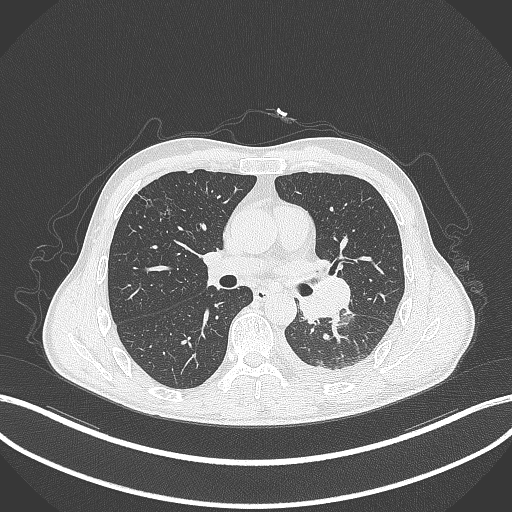
Chest CT, one axial slice. Position 178 of 295 along the scan axis. Reconstruction kernel B70f. Lung window (W 1500 / L -600 HU). 1 mm slice thickness. 512 × 512 image matrix, field of view 400 × 400 mm. Patient: male, 47 years. Case-level facts recorded for this patient, not image findings: clinical TNM (as recorded): T3 N1 M1c; histopathological grade: G3.
Outlined on this slice (bounding box drawn by a radiologist):
- lung tumour (recorded histology: small cell carcinoma): box from (x=296, y=274) to (x=355, y=323) px